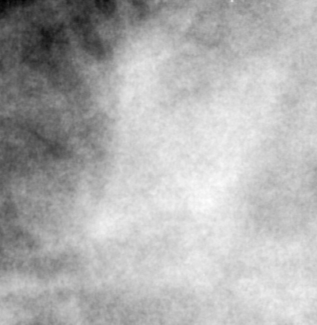
Cropped region of a digitized screen-film mammogram centred on a radiologist-marked abnormality, right breast, CC view, BI-RADS breast density category 4 (scale 1–4).
Marked abnormality: mass, shape architectural distortion, margins spiculated; BI-RADS assessment category 4; subtlety rating 1 on a 1 (subtle) to 5 (obvious) scale; pathology (as recorded): malignant.